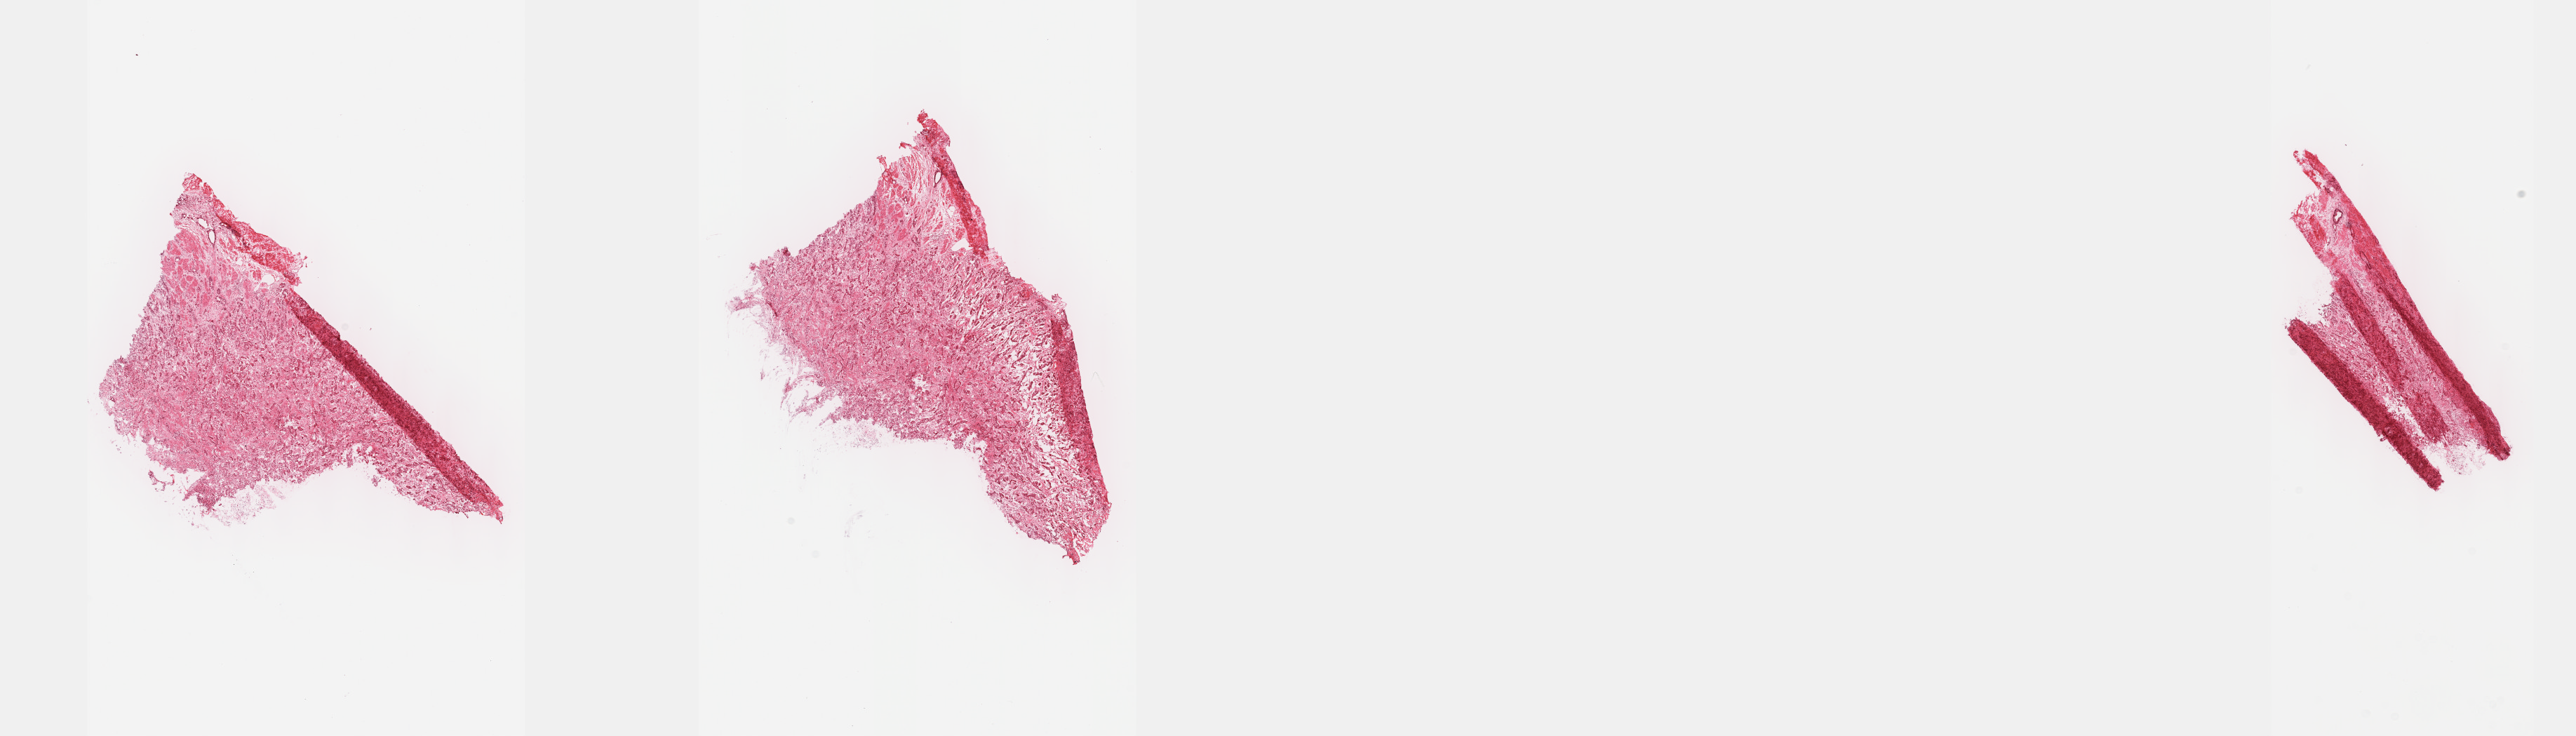
Whole-slide histology image, H&E-stained, a low-resolution overview of the entire scanned area, about 29.7 x 8.5 mm. Frozen section from the top of the tissue portion. Sample: primary tumour, esophagus. Male, age 65 years at initial diagnosis. Histologic grade: G3 (poorly differentiated). Pathologist review of this section (percent, as recorded): tumour cells 60%, tumour nuclei 60%, normal cells 0%, stromal cells 40%, necrosis 0%. Infiltration values recorded for this section: lymphocyte infiltration 40%, monocyte infiltration 20%, neutrophil infiltration 20%.
AJCC pathologic stage: IIIC (7th edition). Histologic diagnosis: Adenocarcinoma, NOS (lower third of esophagus).